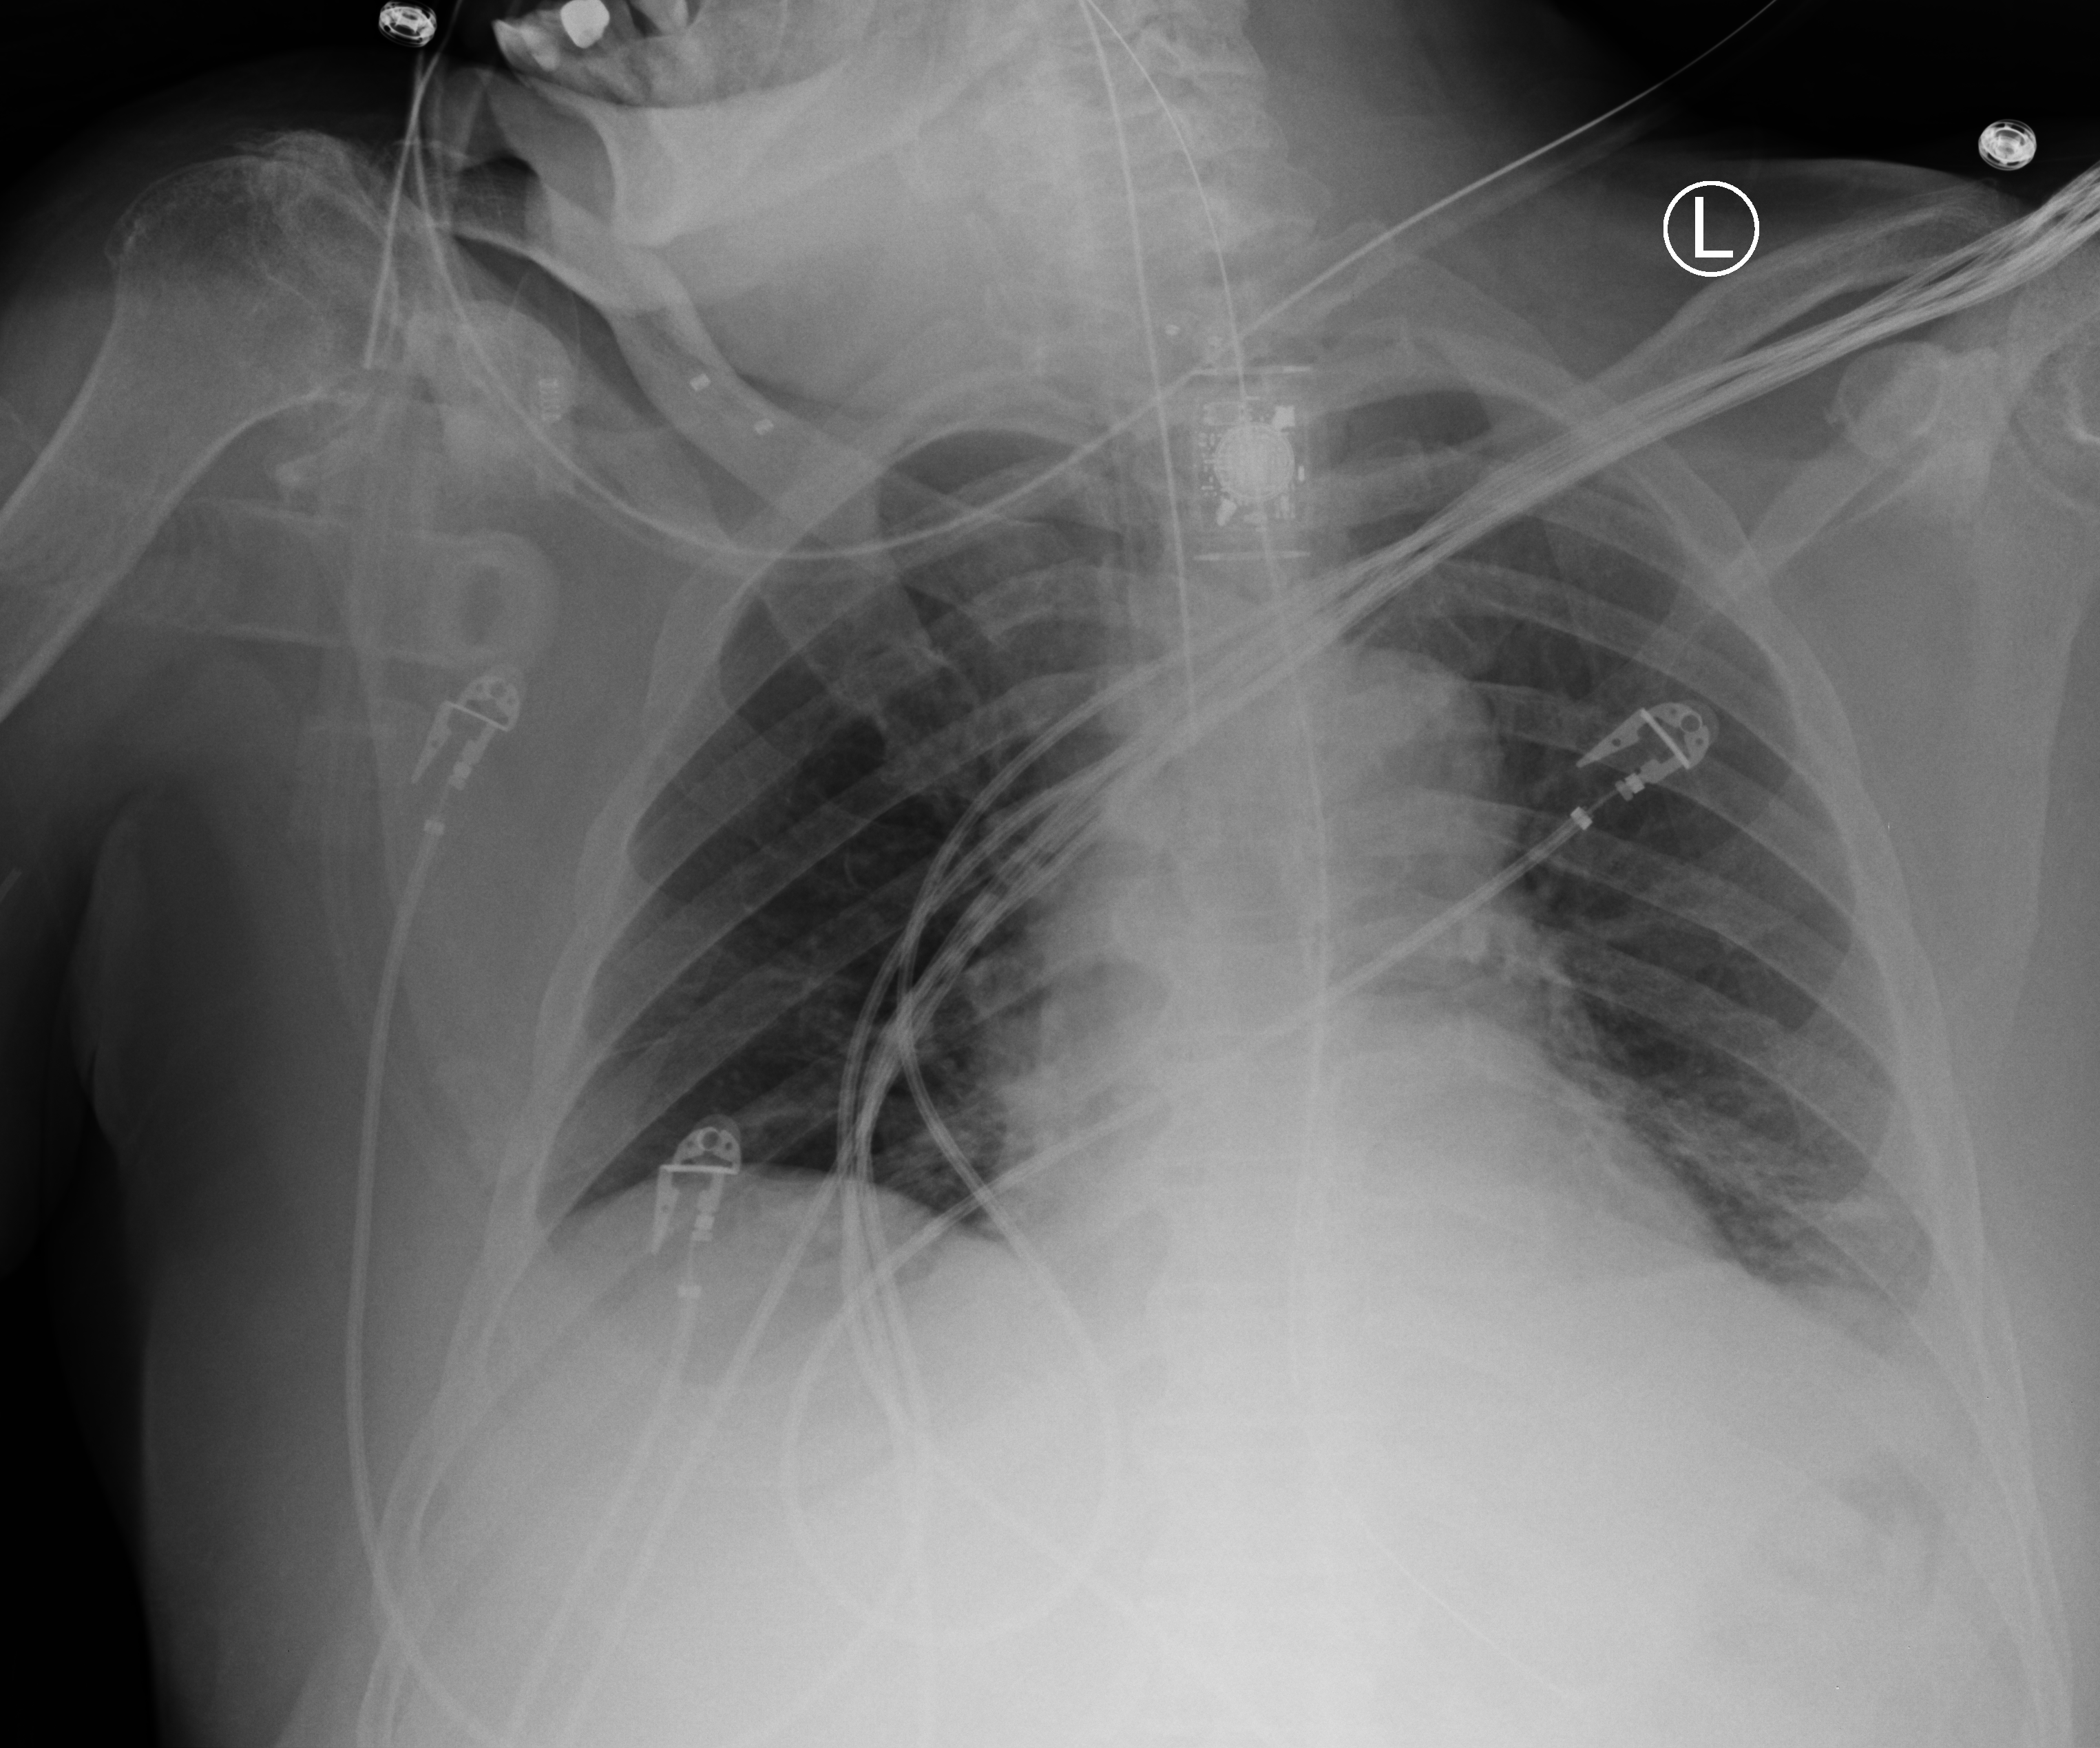
Chest X-ray (portable). Patient hospitalised with COVID-19; male, aged 75–90 years.
Admission-level facts for this patient (not findings on this image; timing relative to this image not recorded): admitted to intensive care during this hospital stay: yes; mechanically ventilated during this hospital stay: yes.